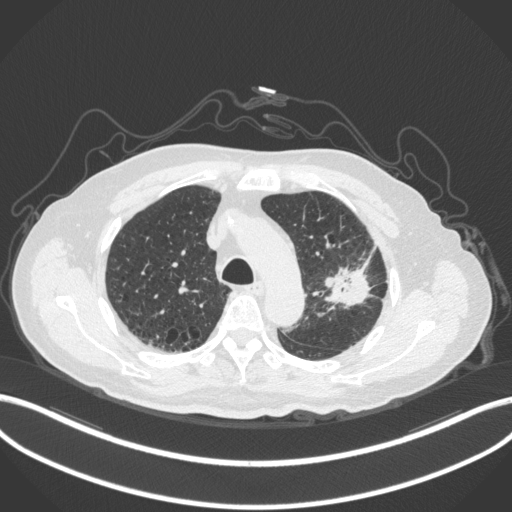
Chest CT, one axial slice; position 220 of 331 along the scan axis; reconstruction kernel B31f; lung window (W 1500 / L -600 HU); 1 mm slice thickness; 512 × 512 image matrix, field of view 400 × 400 mm. Patient: male, 79 years. From the clinical record (not read from this slice): clinical TNM (as recorded): T2a N1 M1; histopathological grade: G3.
Annotated regions visible in this slice (rectangle marked by the reading radiologist):
- lung tumour (recorded histology: adenocarcinoma): bounding box [x1, y1, x2, y2] px = [320, 258, 373, 311]